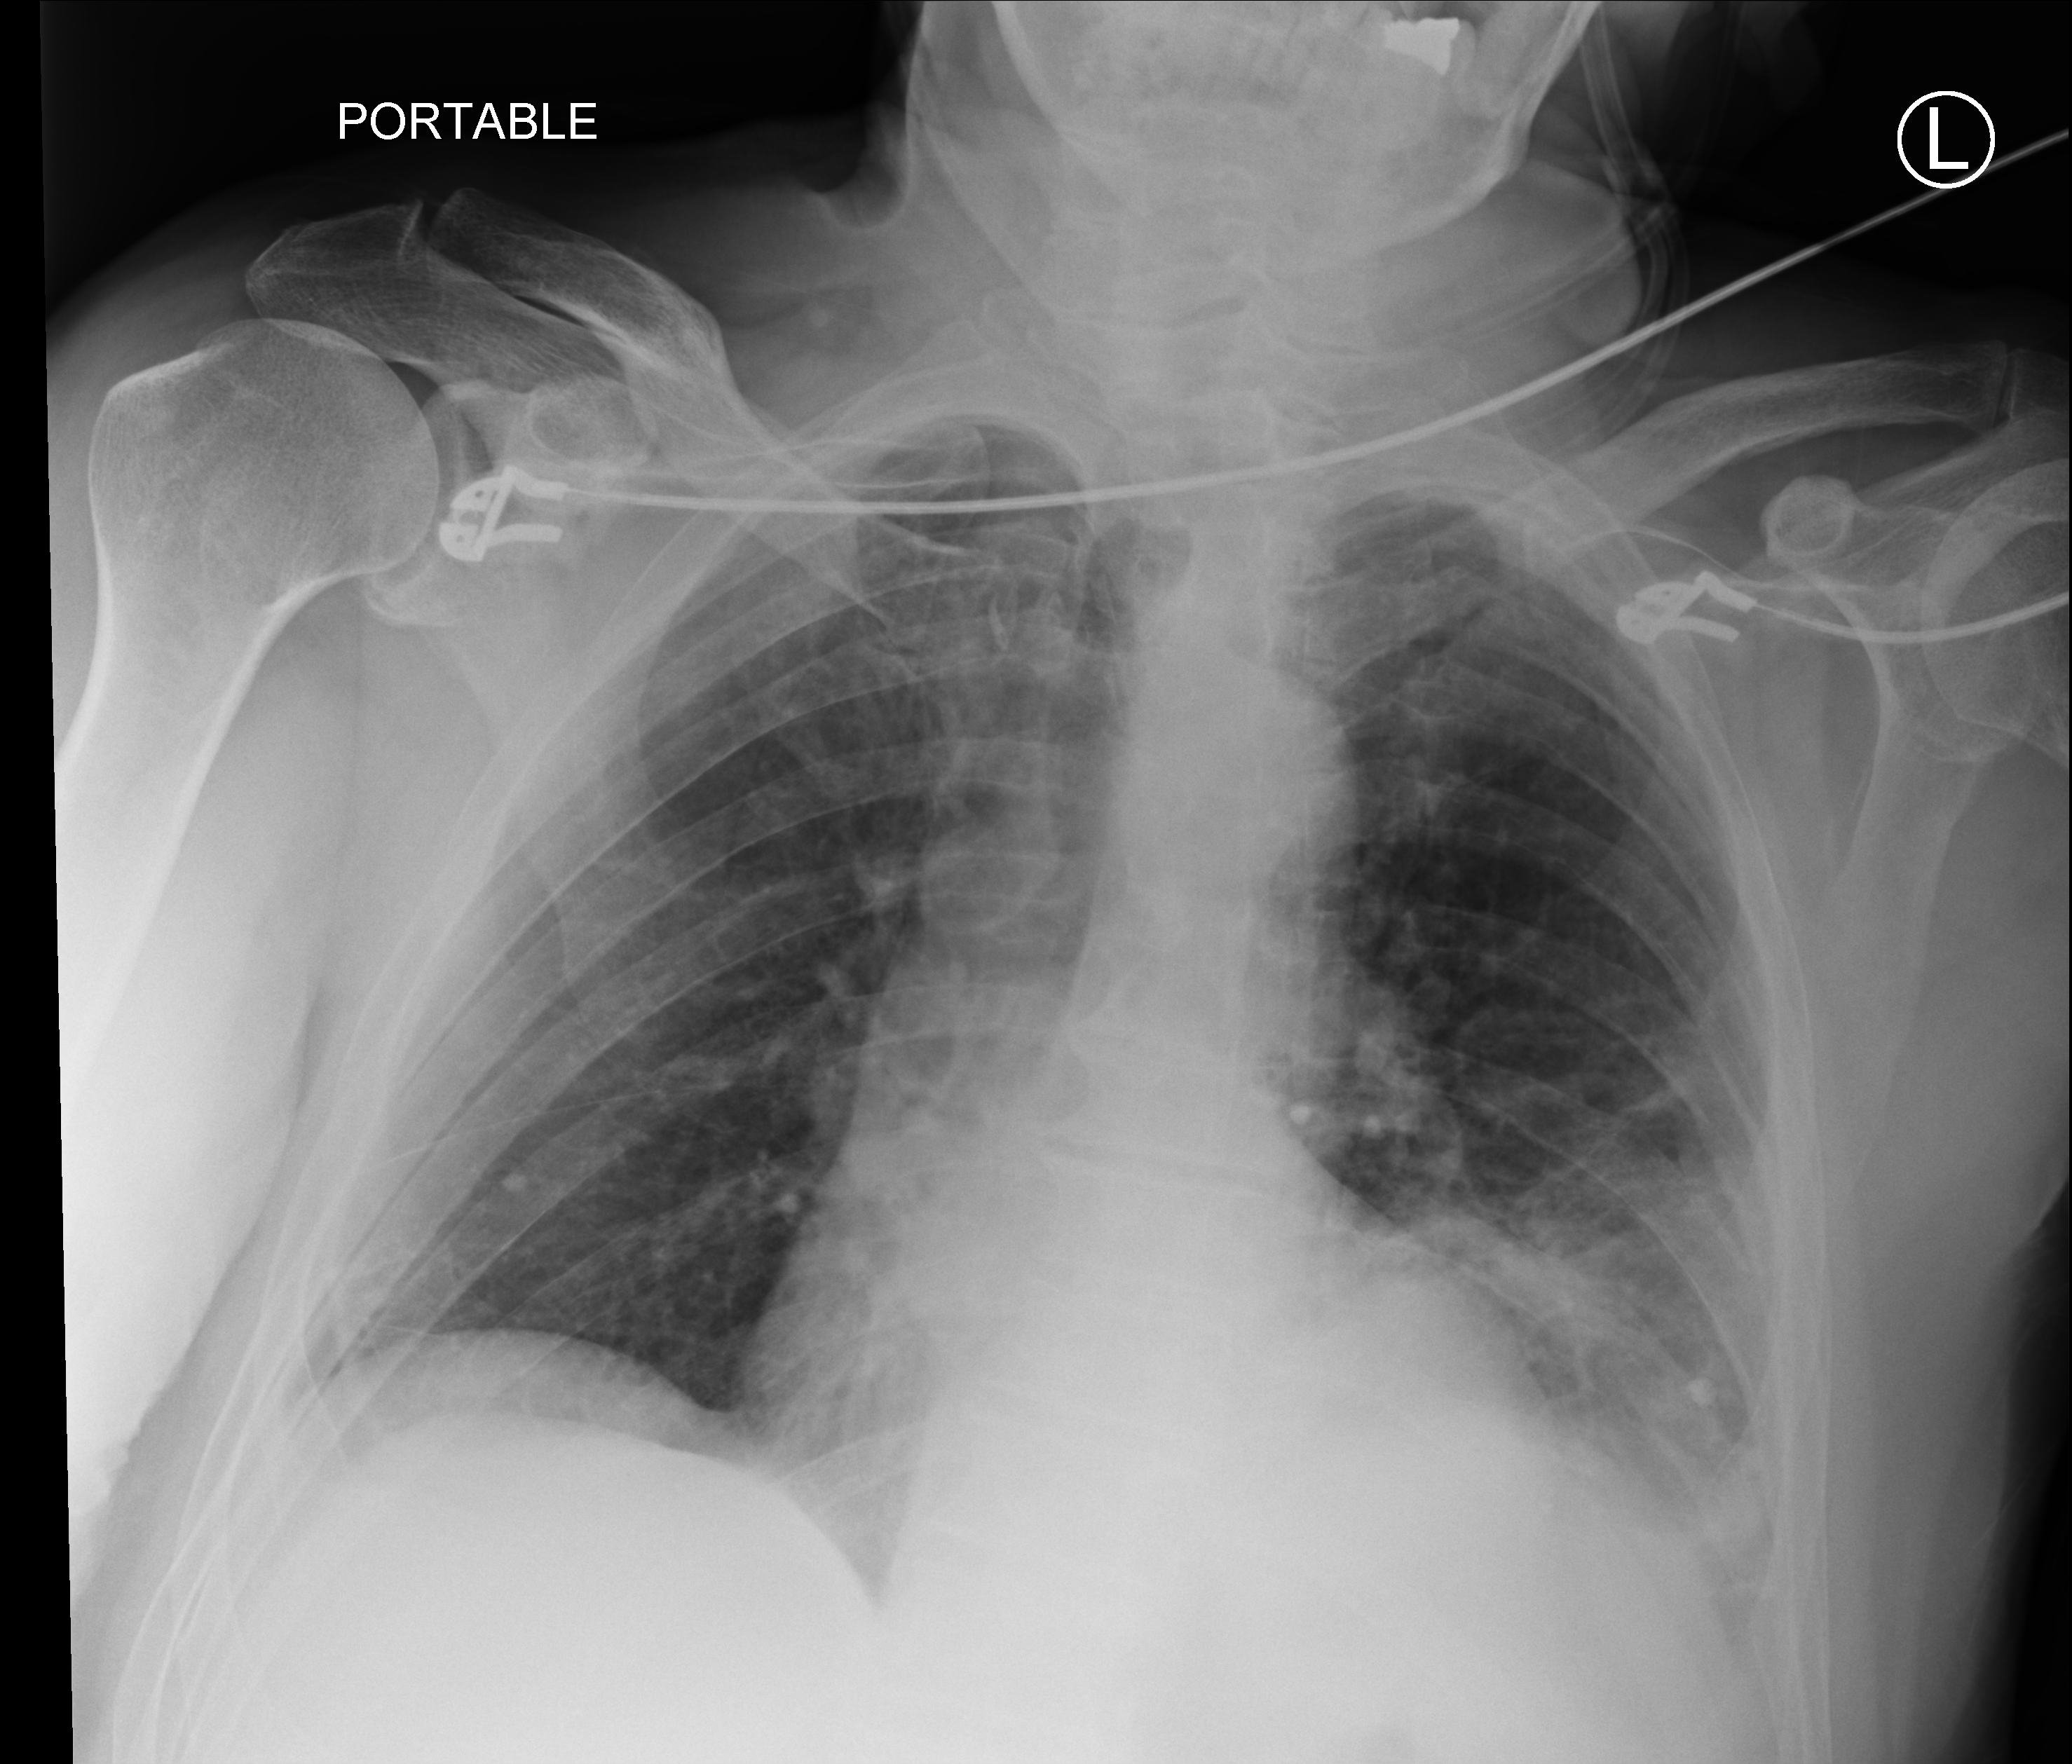
Portable chest radiograph; anteroposterior (AP) projection. Patient hospitalised with COVID-19; male, aged 75–90 years.
Hospital-stay facts (about this admission, not read from this image; timing relative to this image not recorded): admitted to intensive care during this hospital stay: no.